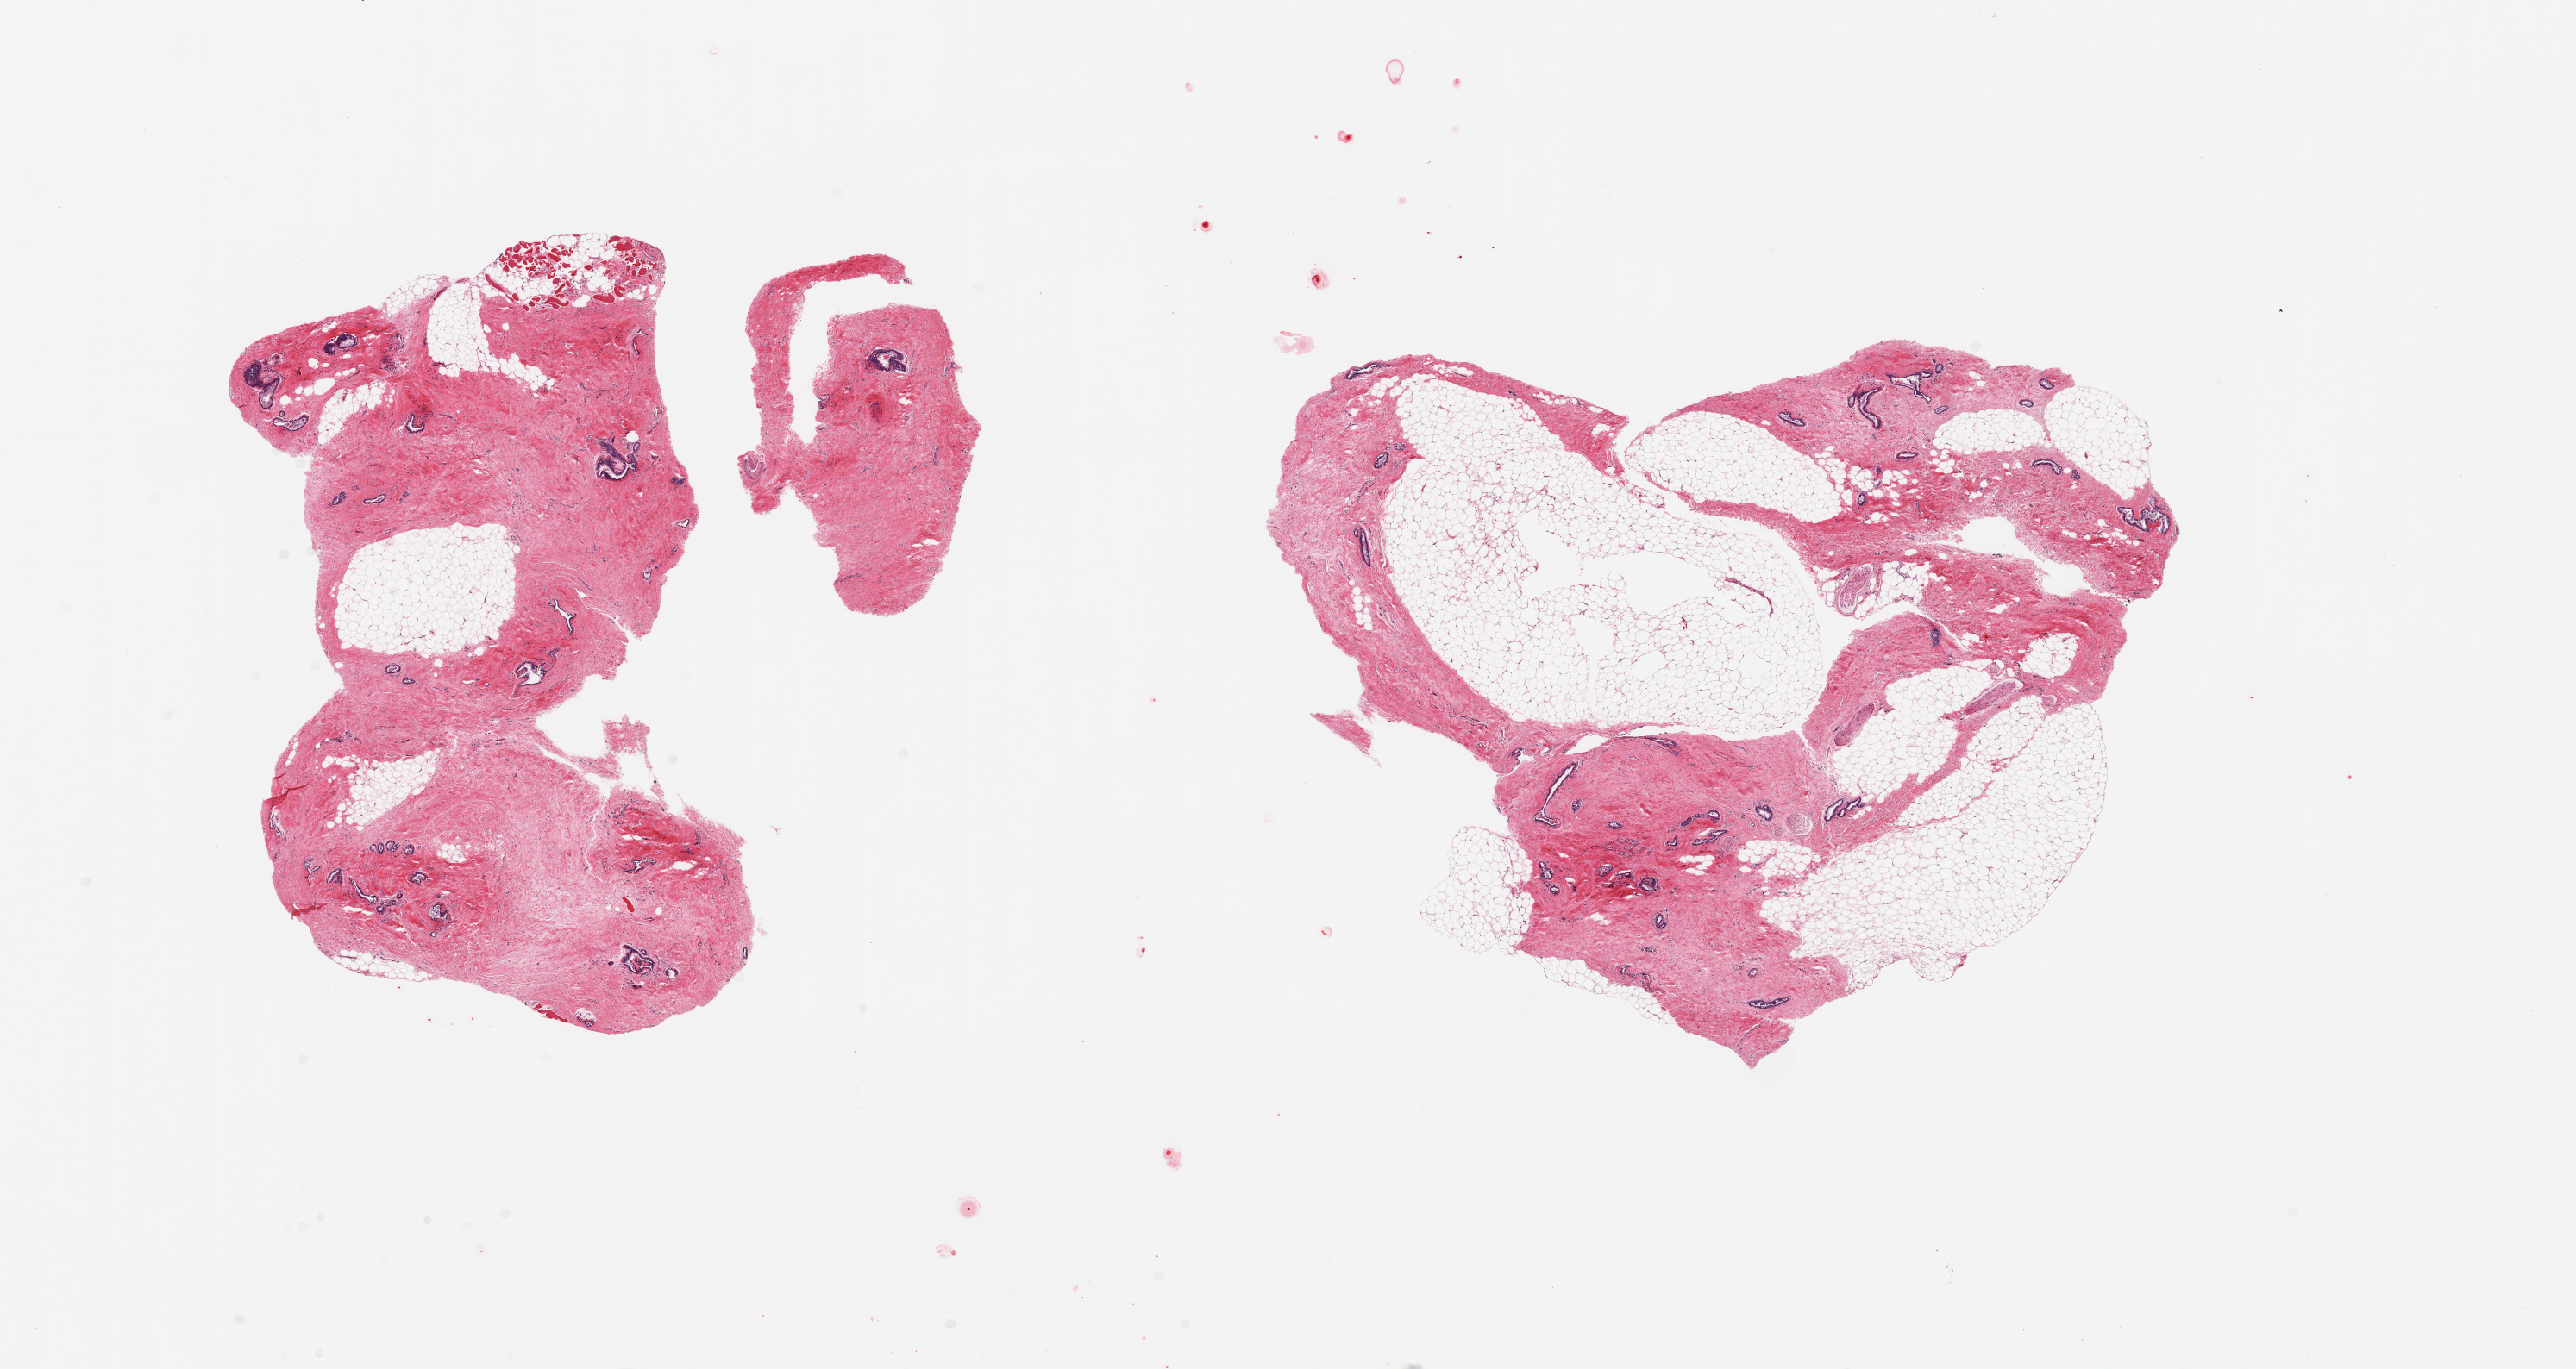
Digitized hematoxylin and eosin (H&E)-stained section, a low-resolution overview of the entire scanned area, about 23.6 x 12.6 mm (slide scanned at 20x). PAXgene-fixed paraffin-embedded (PFPE) section. Target tissue: breast. Tissue donor sample. Donor: male.
Review note (as recorded): 2 pieces; fat and dense stroma with multiple embedded ducts, some gynecomastoid change.